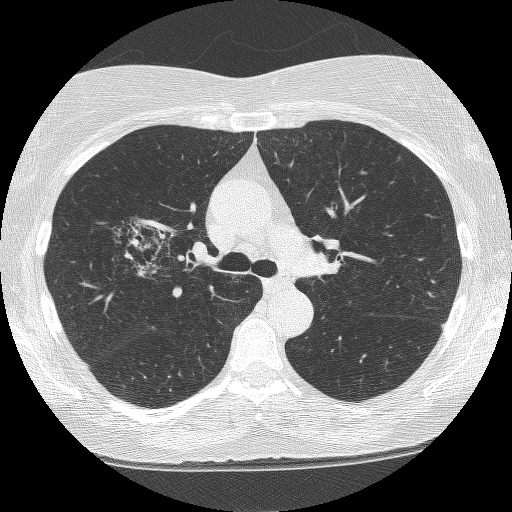
Axial slice from a low-dose chest CT screening exam. Second annual screen. Lung window (W 1500 / L -600 HU). 1.25 mm slice thickness. Lung (sharp) reconstruction kernel (BONE). Female, age 64 years at enrolment.
Expert-annotated lung lesion, bounding box (x1, y1, x2, y2) in pixels: (115, 204, 209, 292). The screening reader recorded 4 non-calcified nodules or masses ≥4 mm on this exam (right upper lobe, right upper lobe, right upper lobe, left upper lobe); which of them this box marks is not recorded. Official screen result: positive, other. Participant outcome: lung cancer diagnosed 381 days after this screen — adenocarcinoma, NOS, right upper lobe, right middle lobe, right hilum, stage IV (AJCC 6th edition), 85 mm at pathology.